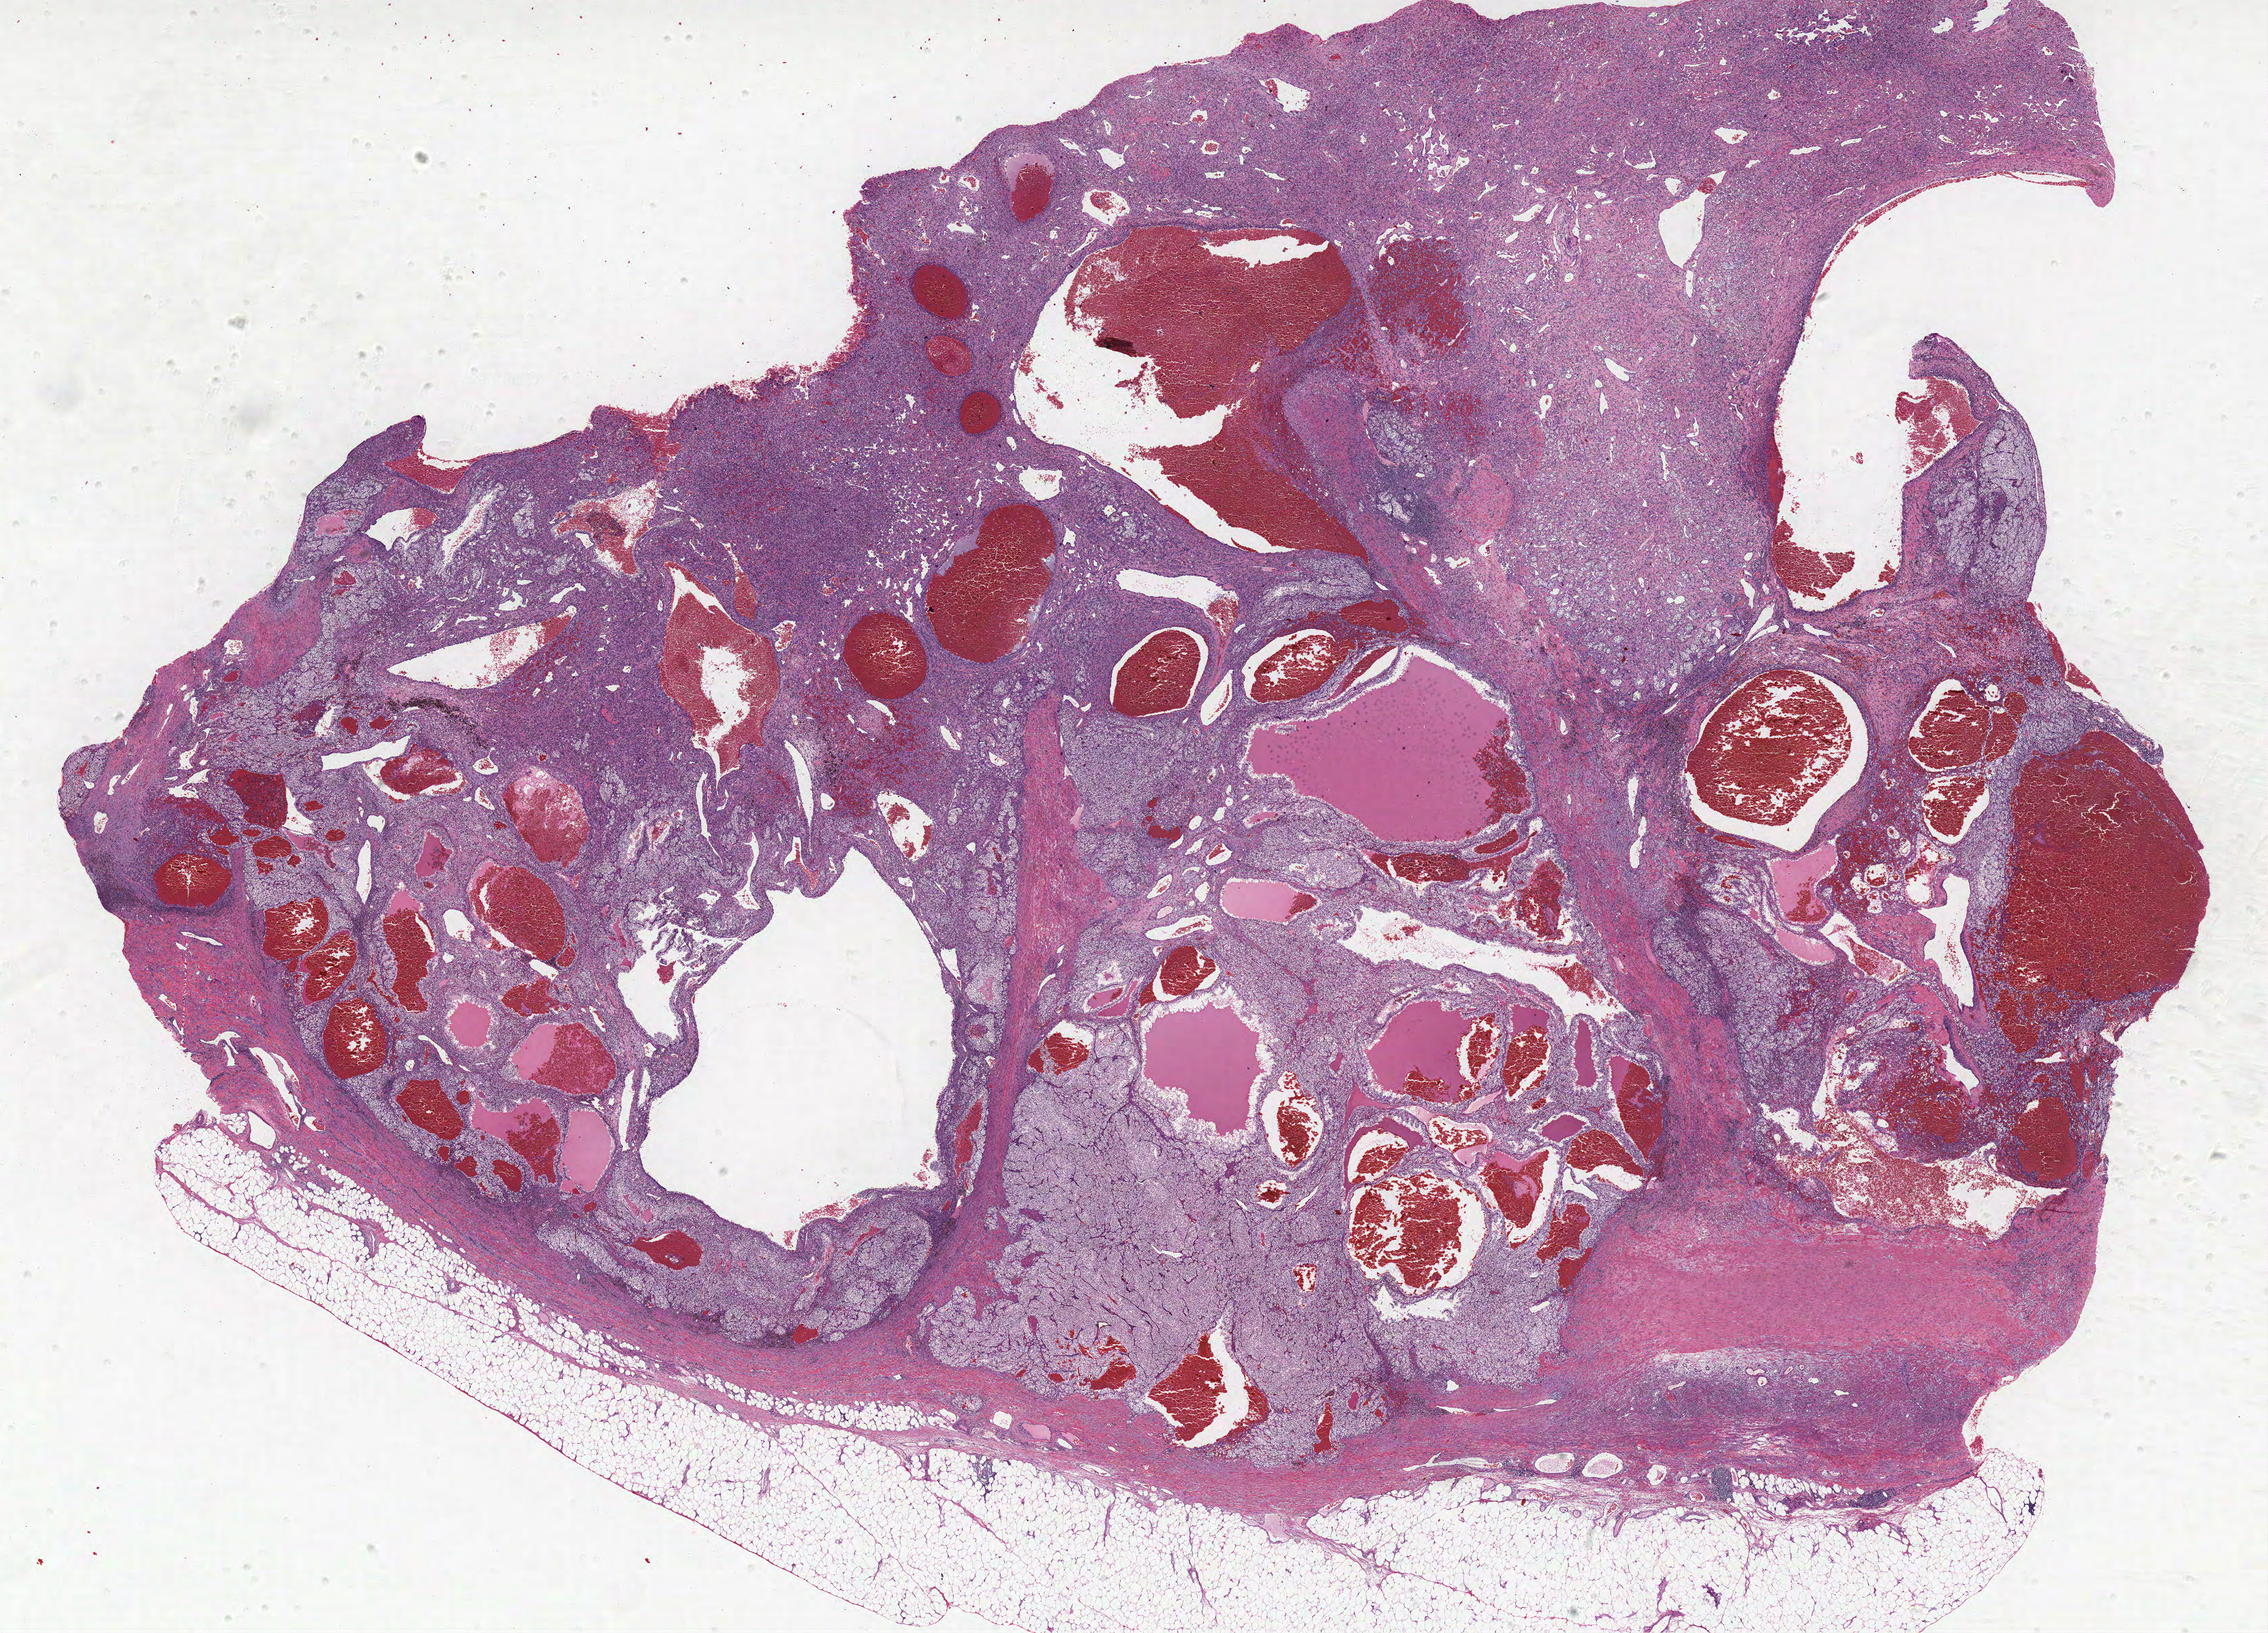
Digitized H&E tissue section (whole slide) — shown as a low-resolution overview of the whole scanned area (about 26.6 x 19.2 mm). FFPE section. Sample: primary tumour, kidney. Patient: male, age at initial diagnosis 58 years. Histologic grade: G4 (undifferentiated).
- lymph nodes positive (case pathology): 0 of 4 examined
- AJCC pathologic stage: II
- diagnosis: Clear cell adenocarcinoma, NOS
- laterality: left